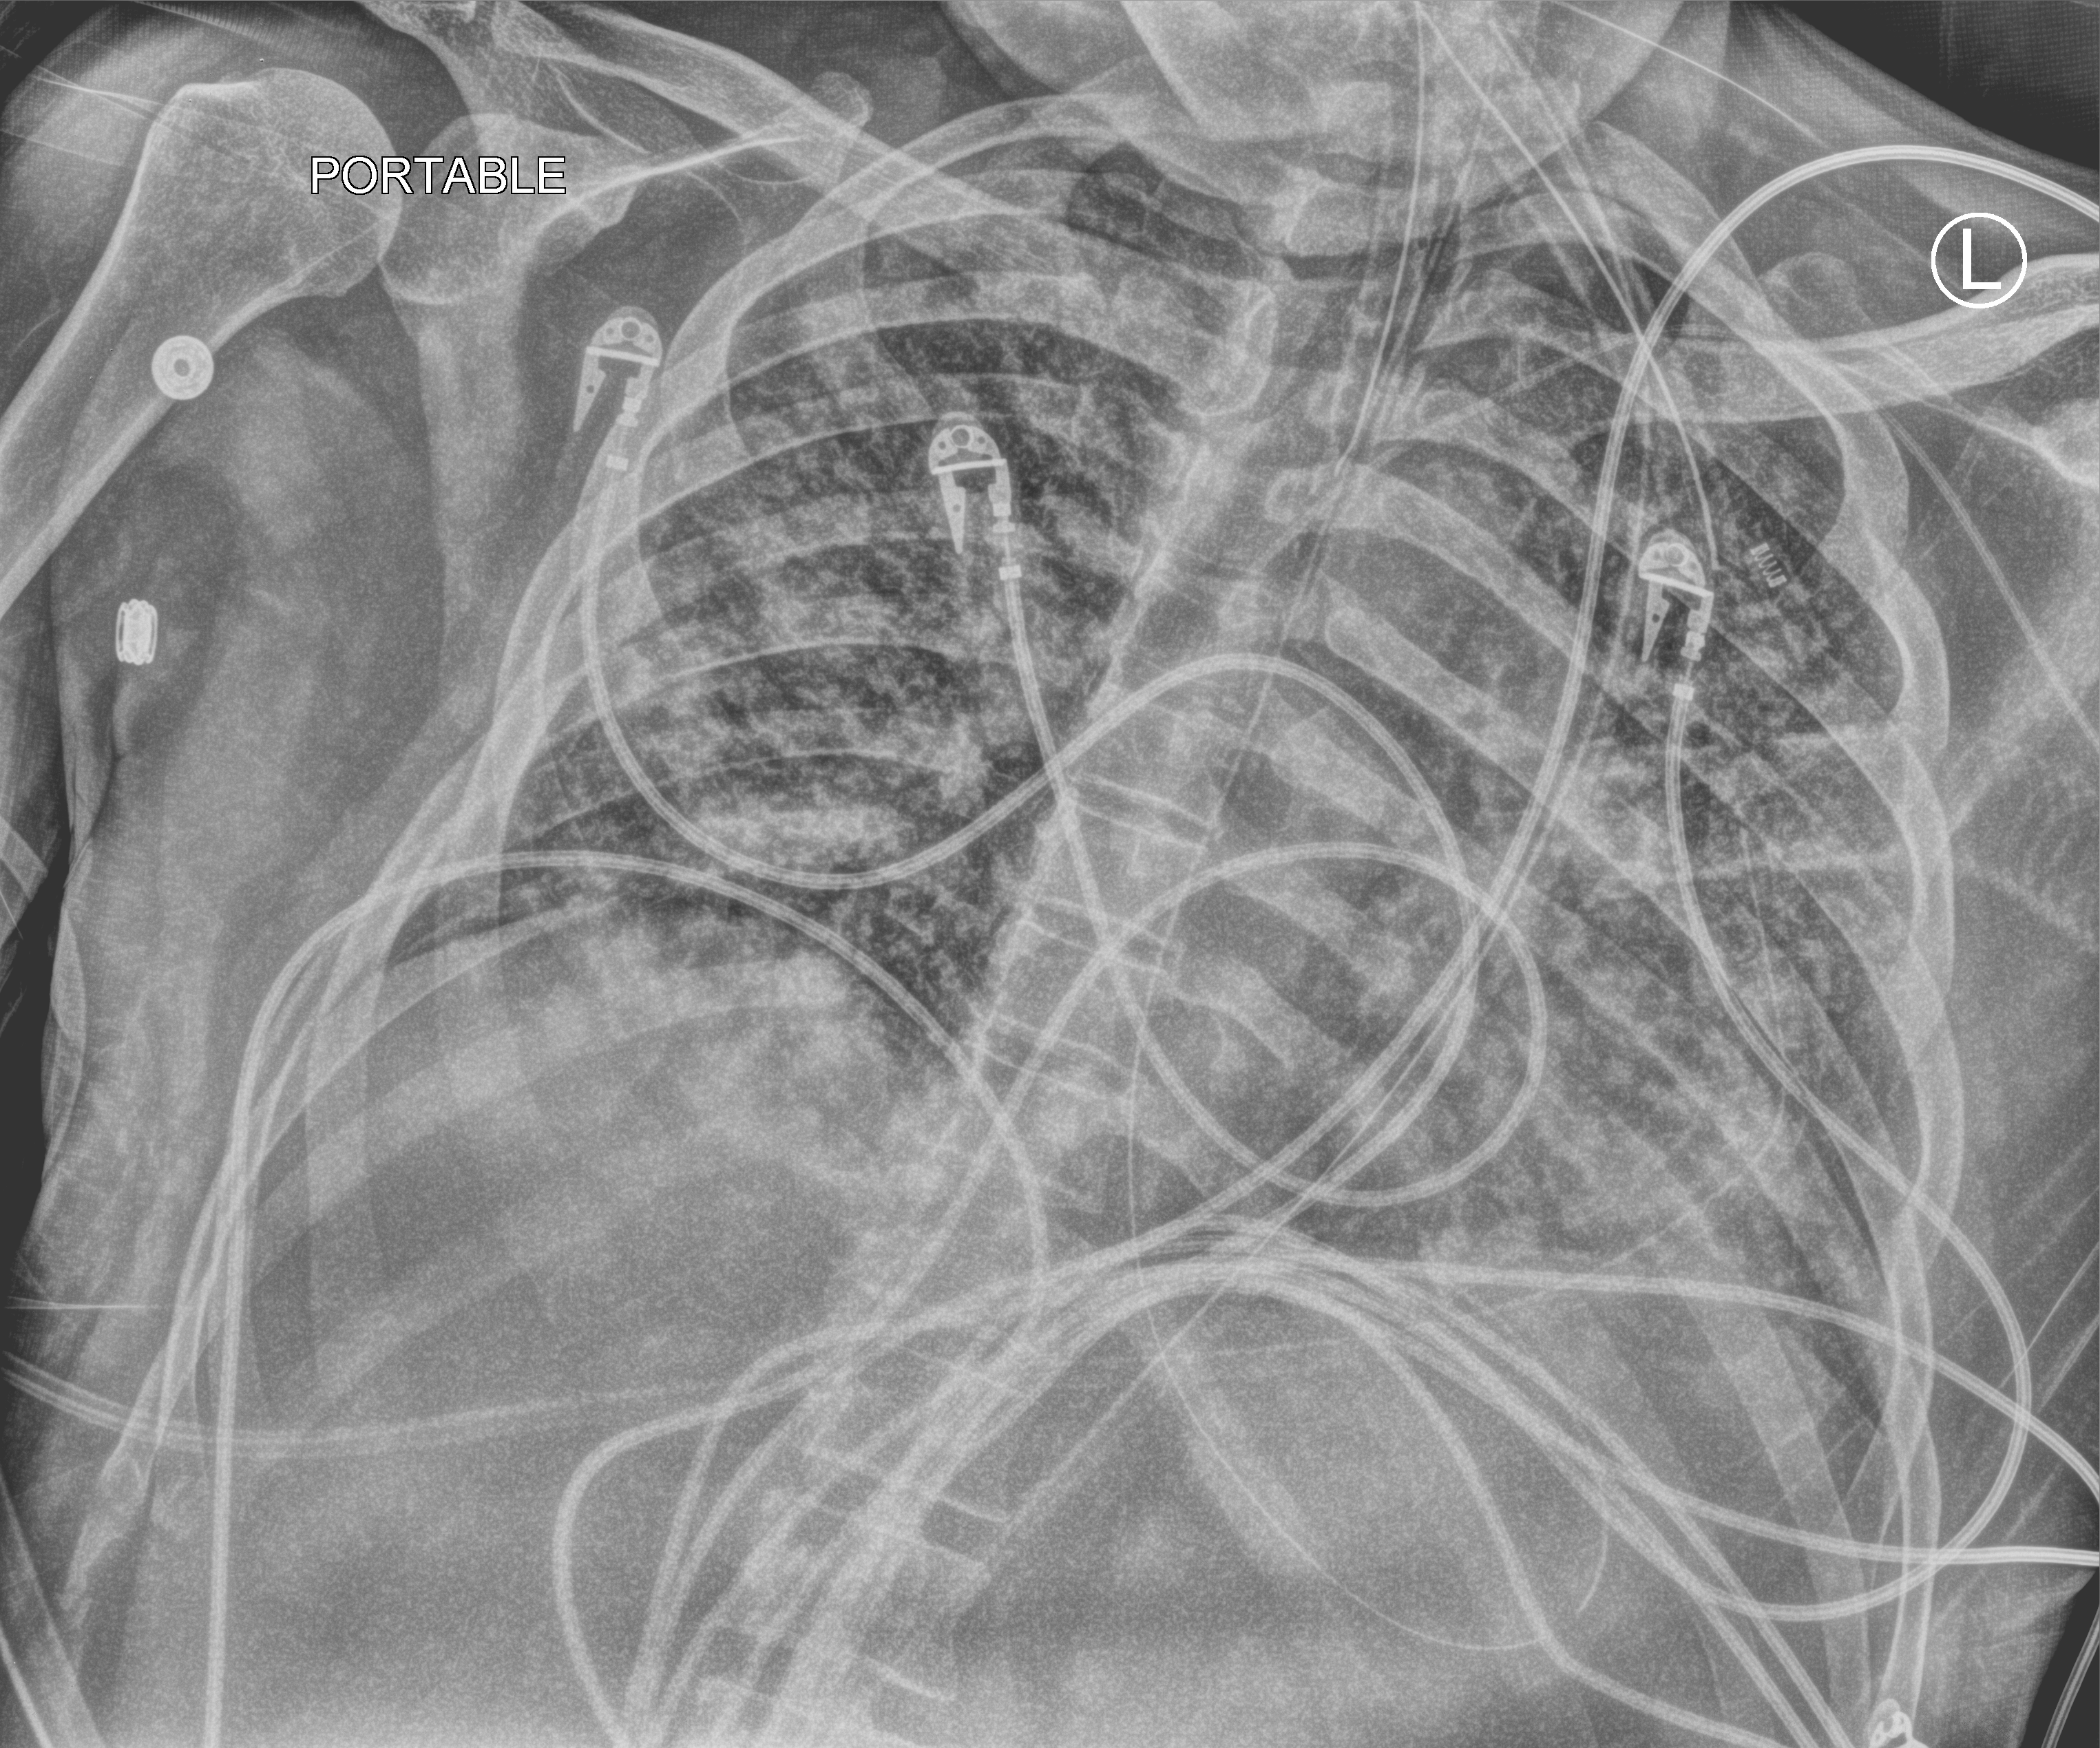
Chest X-ray (portable). Male patient hospitalised with COVID-19, age 18–59 years.
Admission-level facts for this patient (not findings on this image; timing relative to this image not recorded): hypertension (admission record): no.